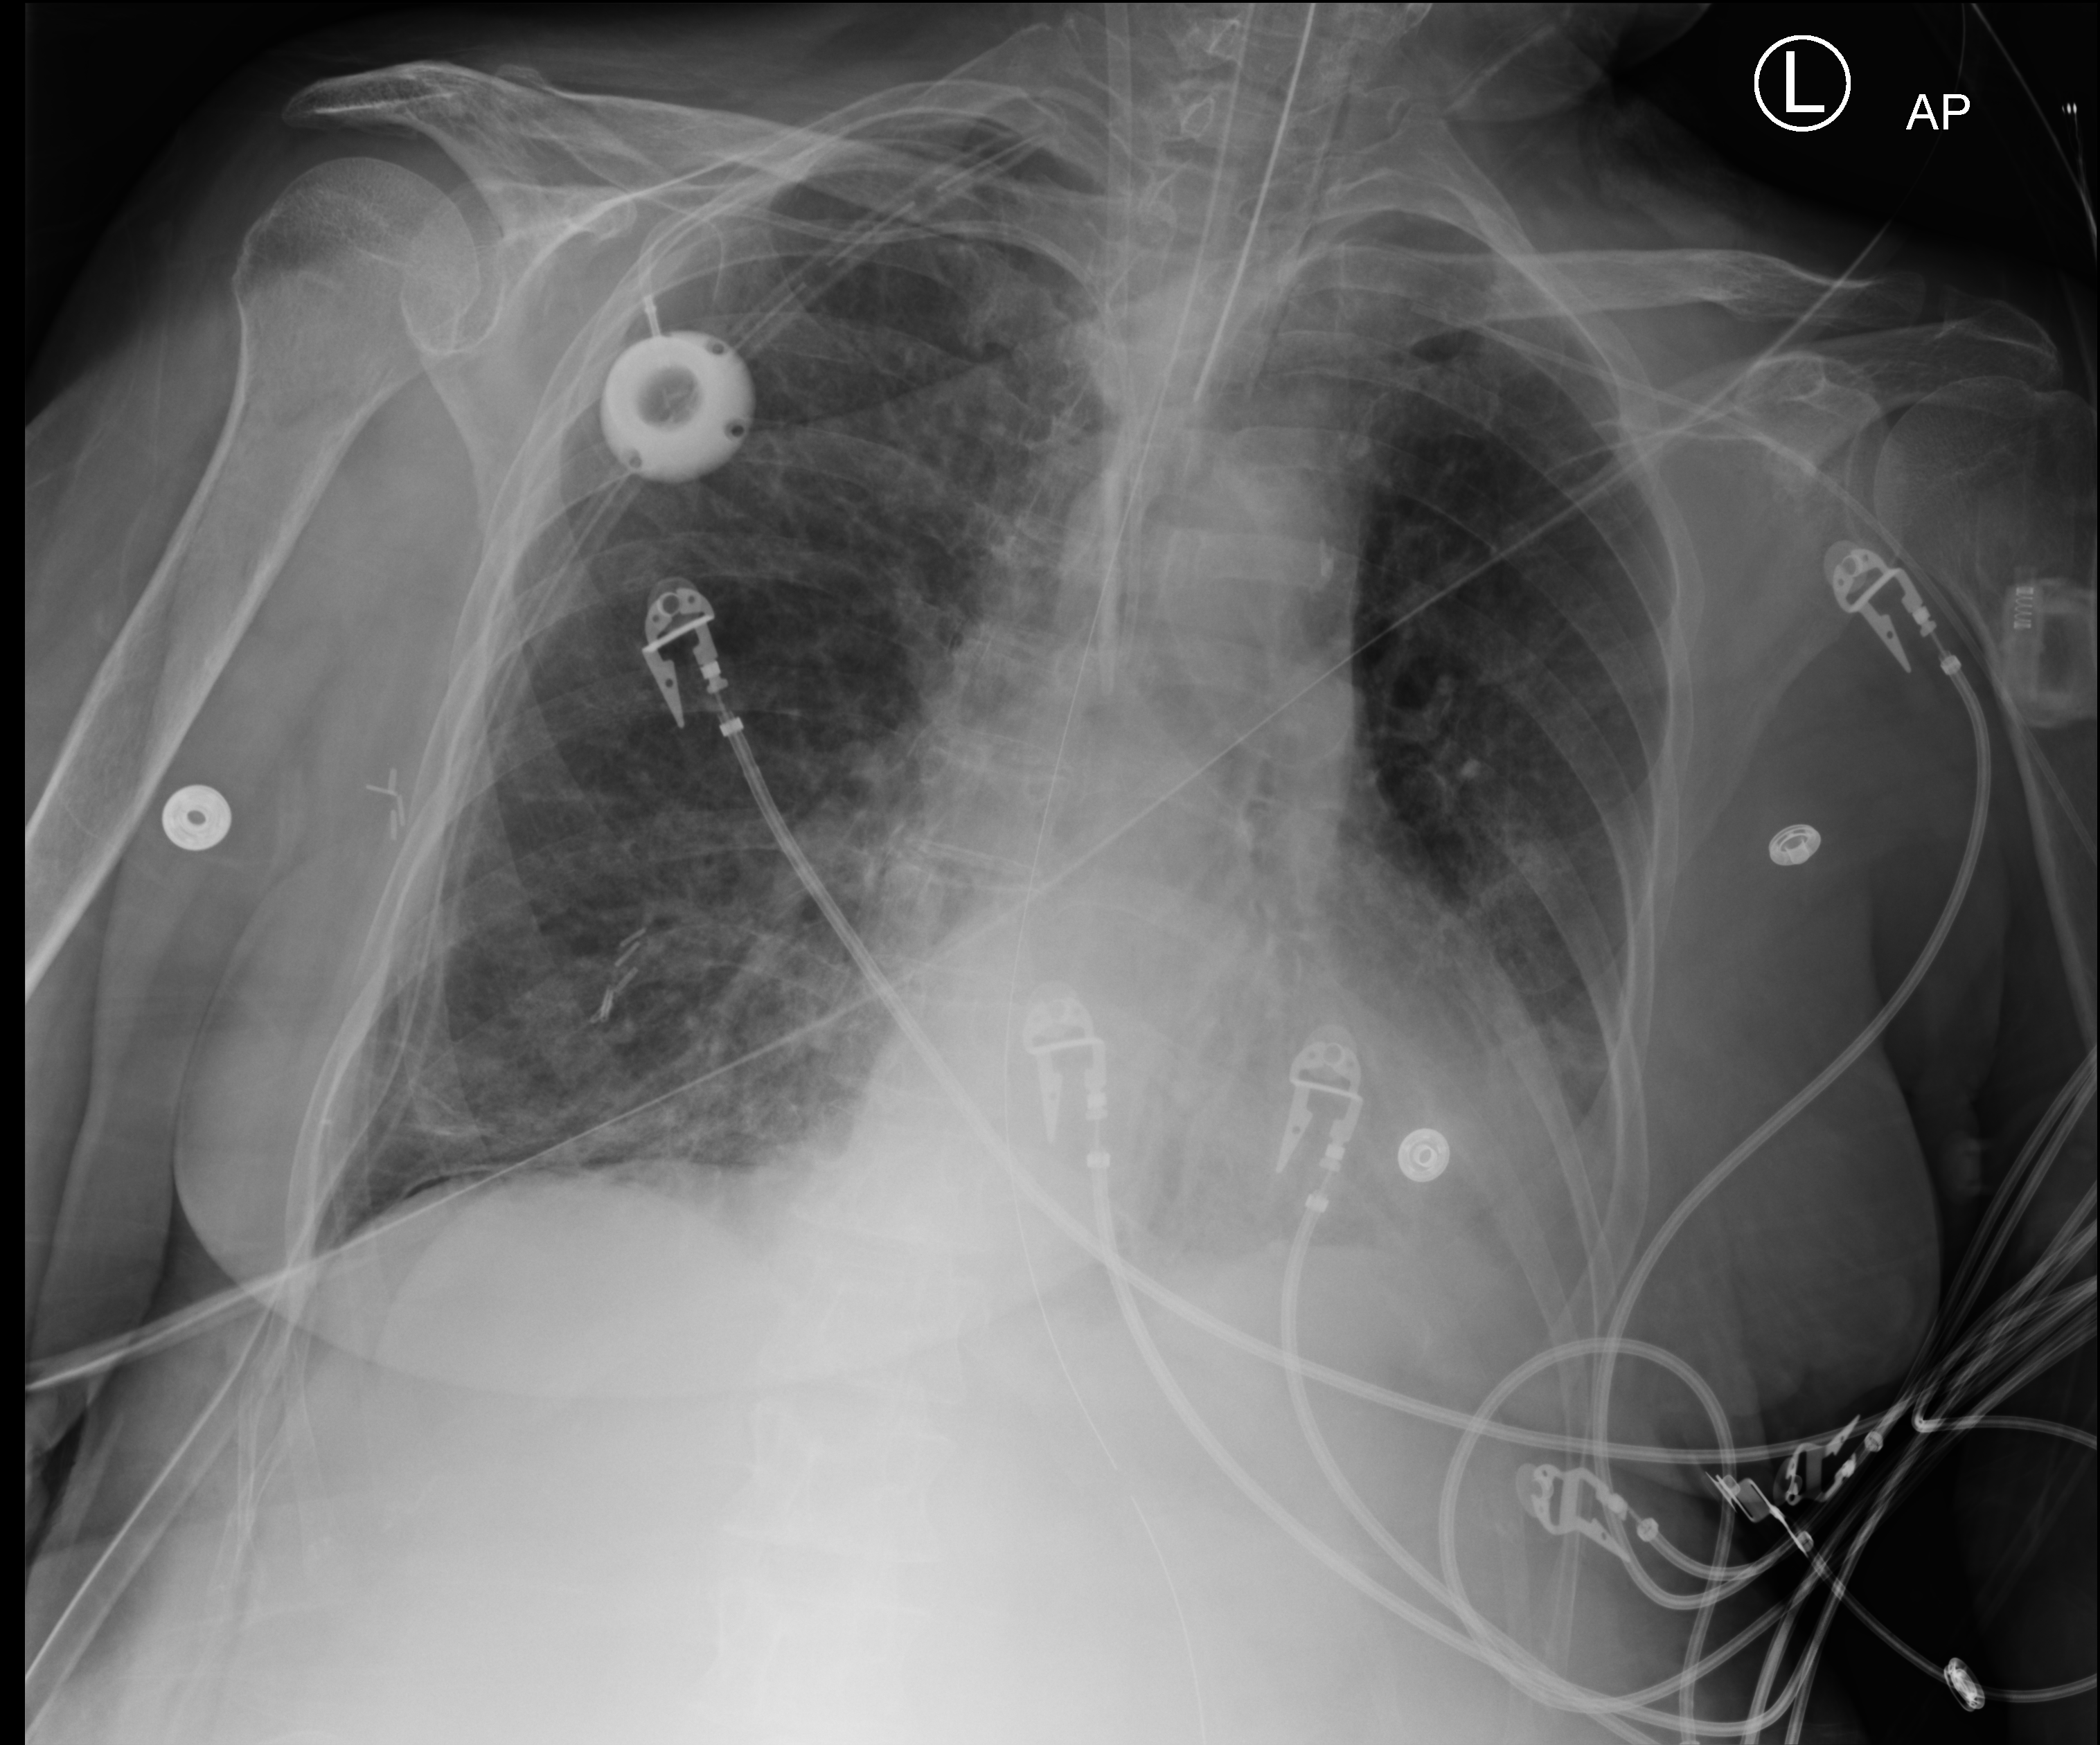
Bedside chest radiograph (computed radiography). Patient hospitalised with COVID-19; female, aged 60–74 years.
From the hospital-stay record, not from the radiograph (when in the stay this image was taken is not recorded):
- admitted to intensive care during this hospital stay: yes